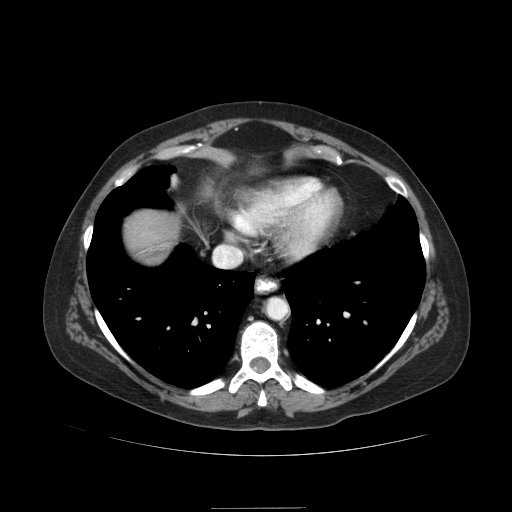
Contrast-enhanced abdominal CT (liver protocol), one axial slice; slice 80 of 89 in the series (ordered by position); soft-tissue window (W 400 / L 40 HU); 512 × 512 image matrix, field of view 400 × 400 mm. From the clinical record (not read from this slice): diagnosis: hepatocellular carcinoma (patient treated with transarterial chemoembolisation; whether this scan precedes or follows treatment is not stated here); TNM stage (as recorded): Stage-IIIB; Child-Pugh class: A.
Outlined on this slice (semi-automatically segmented with operator editing):
- liver parenchyma outside the tumour (the mass and vessels are separate outlines, so this box may not span the whole liver): bounding box [x1, y1, x2, y2] px = [126, 212, 178, 253]